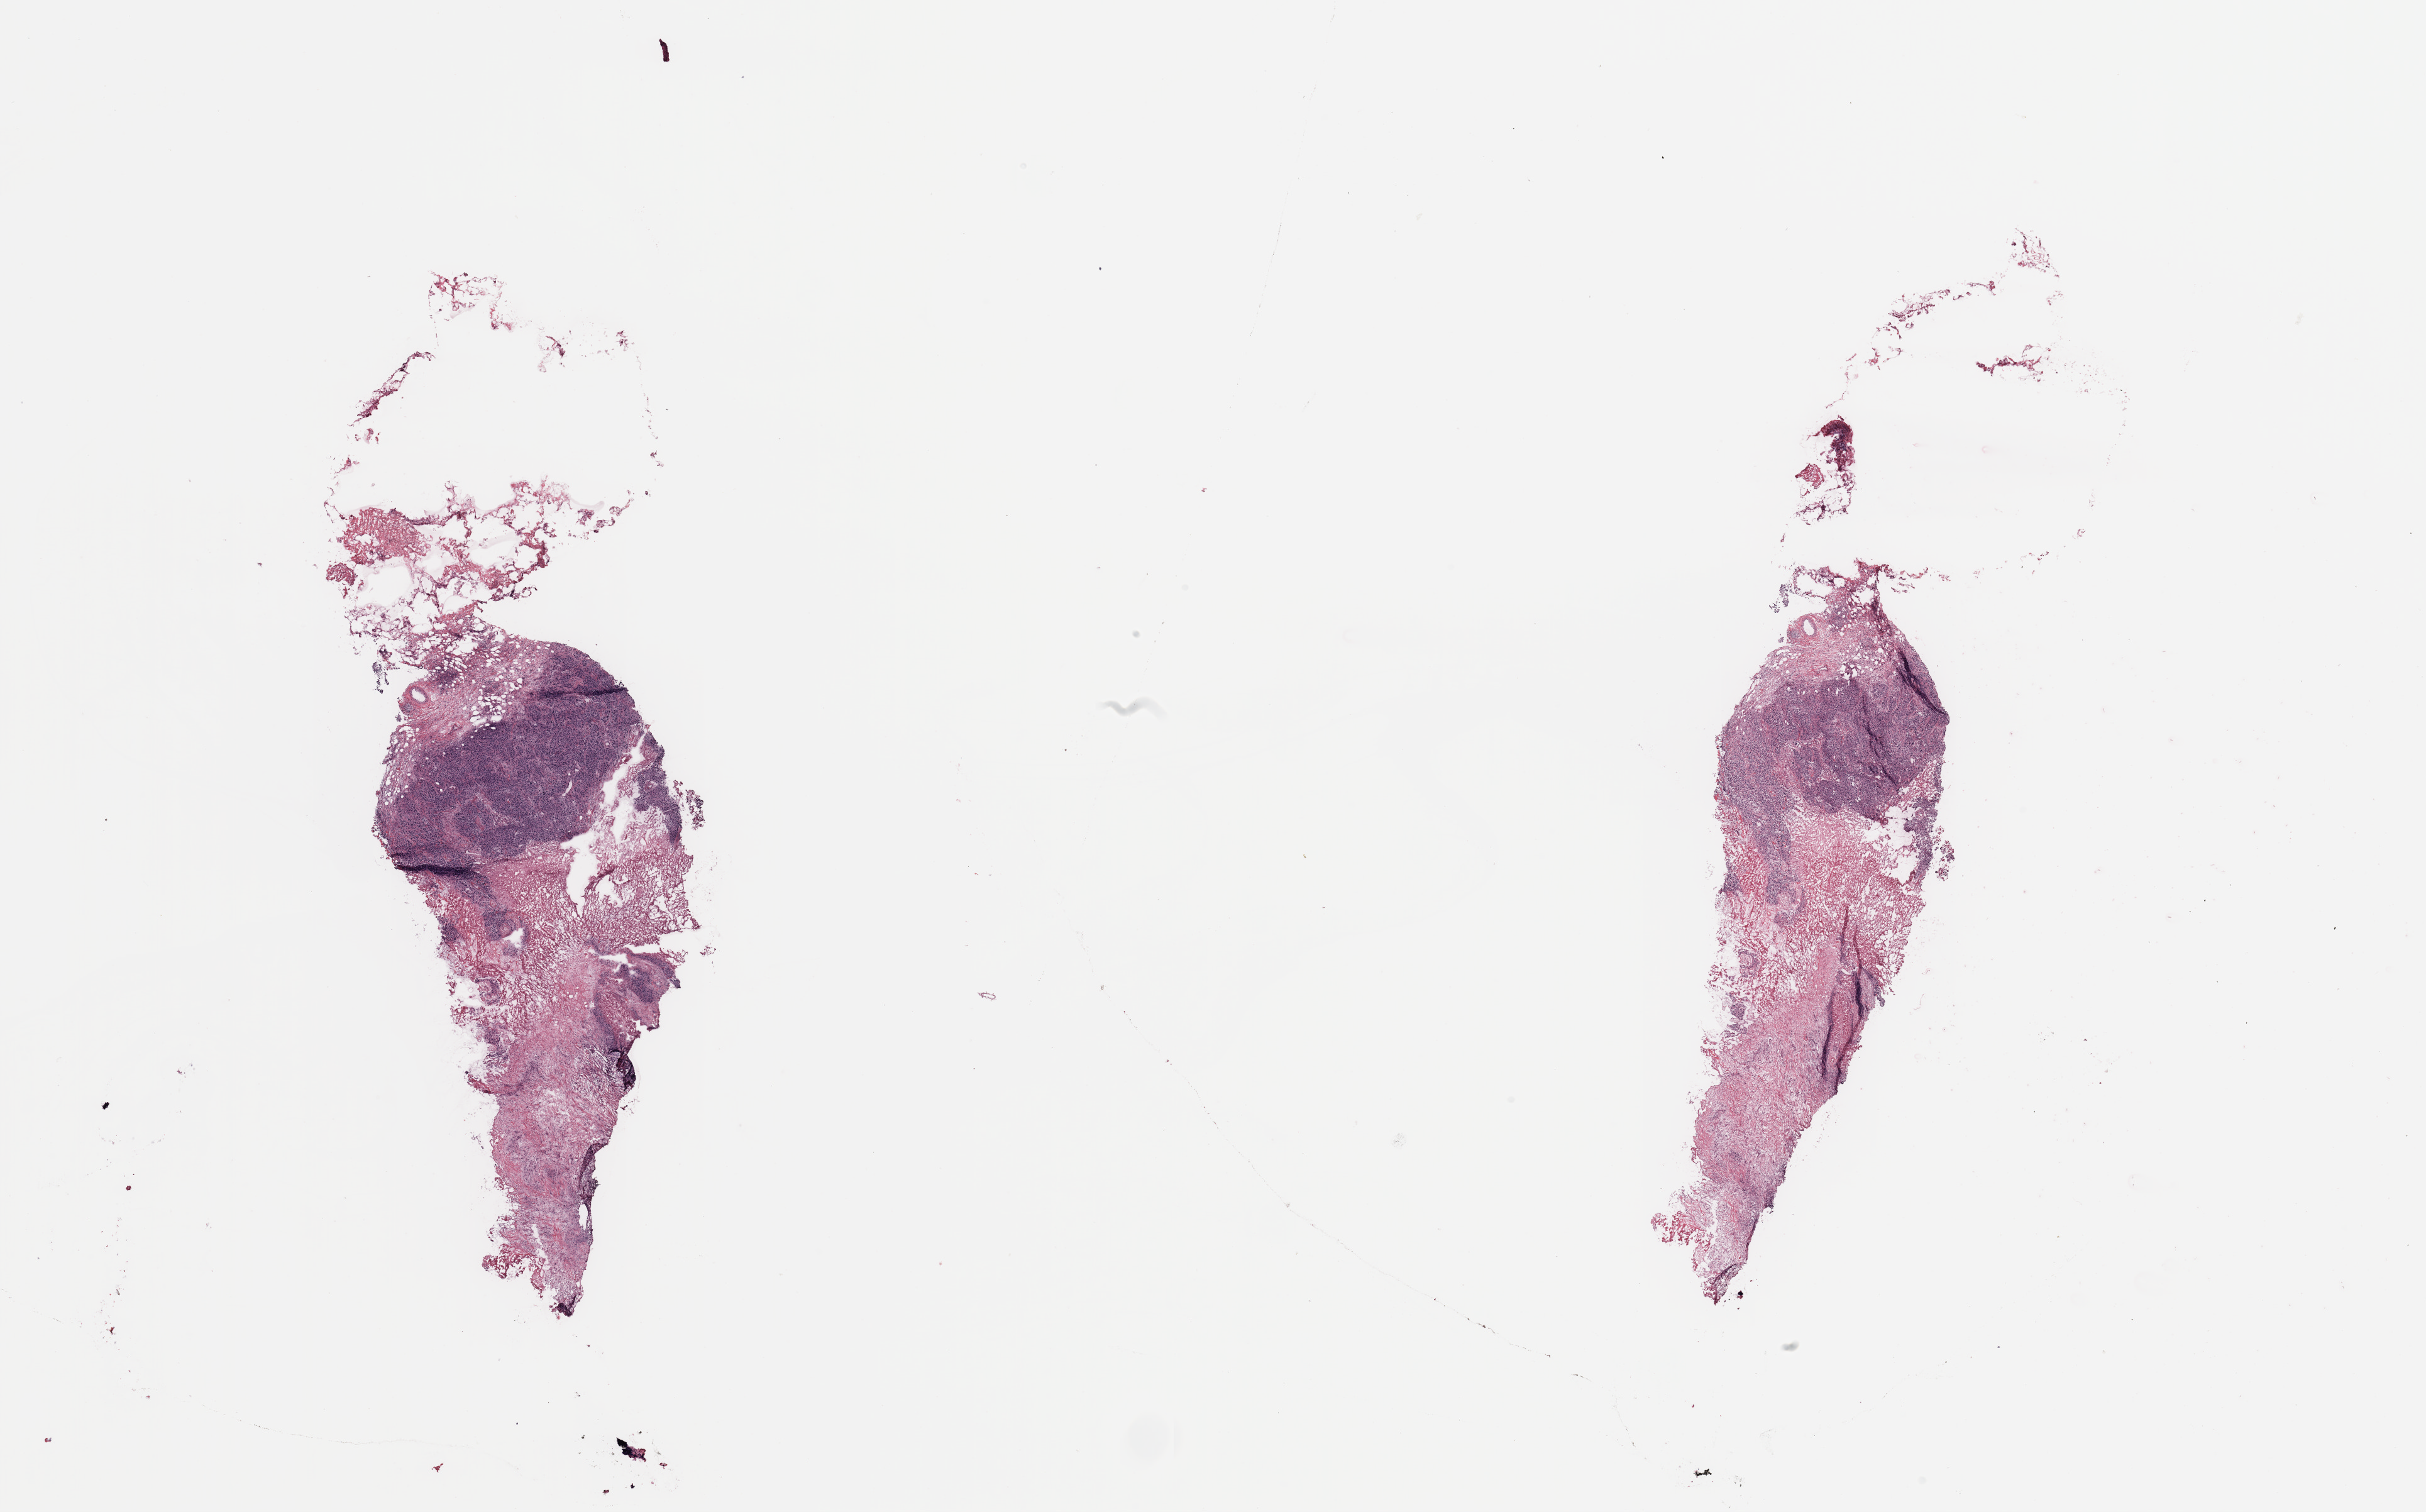
H&E-stained whole-slide image, whole scanned area (about 30.5 x 19.0 mm) shown as a low-resolution overview. Breast, tissue type not recorded.
Patient diagnosis (cohort enrolment): breast cancer (breast).